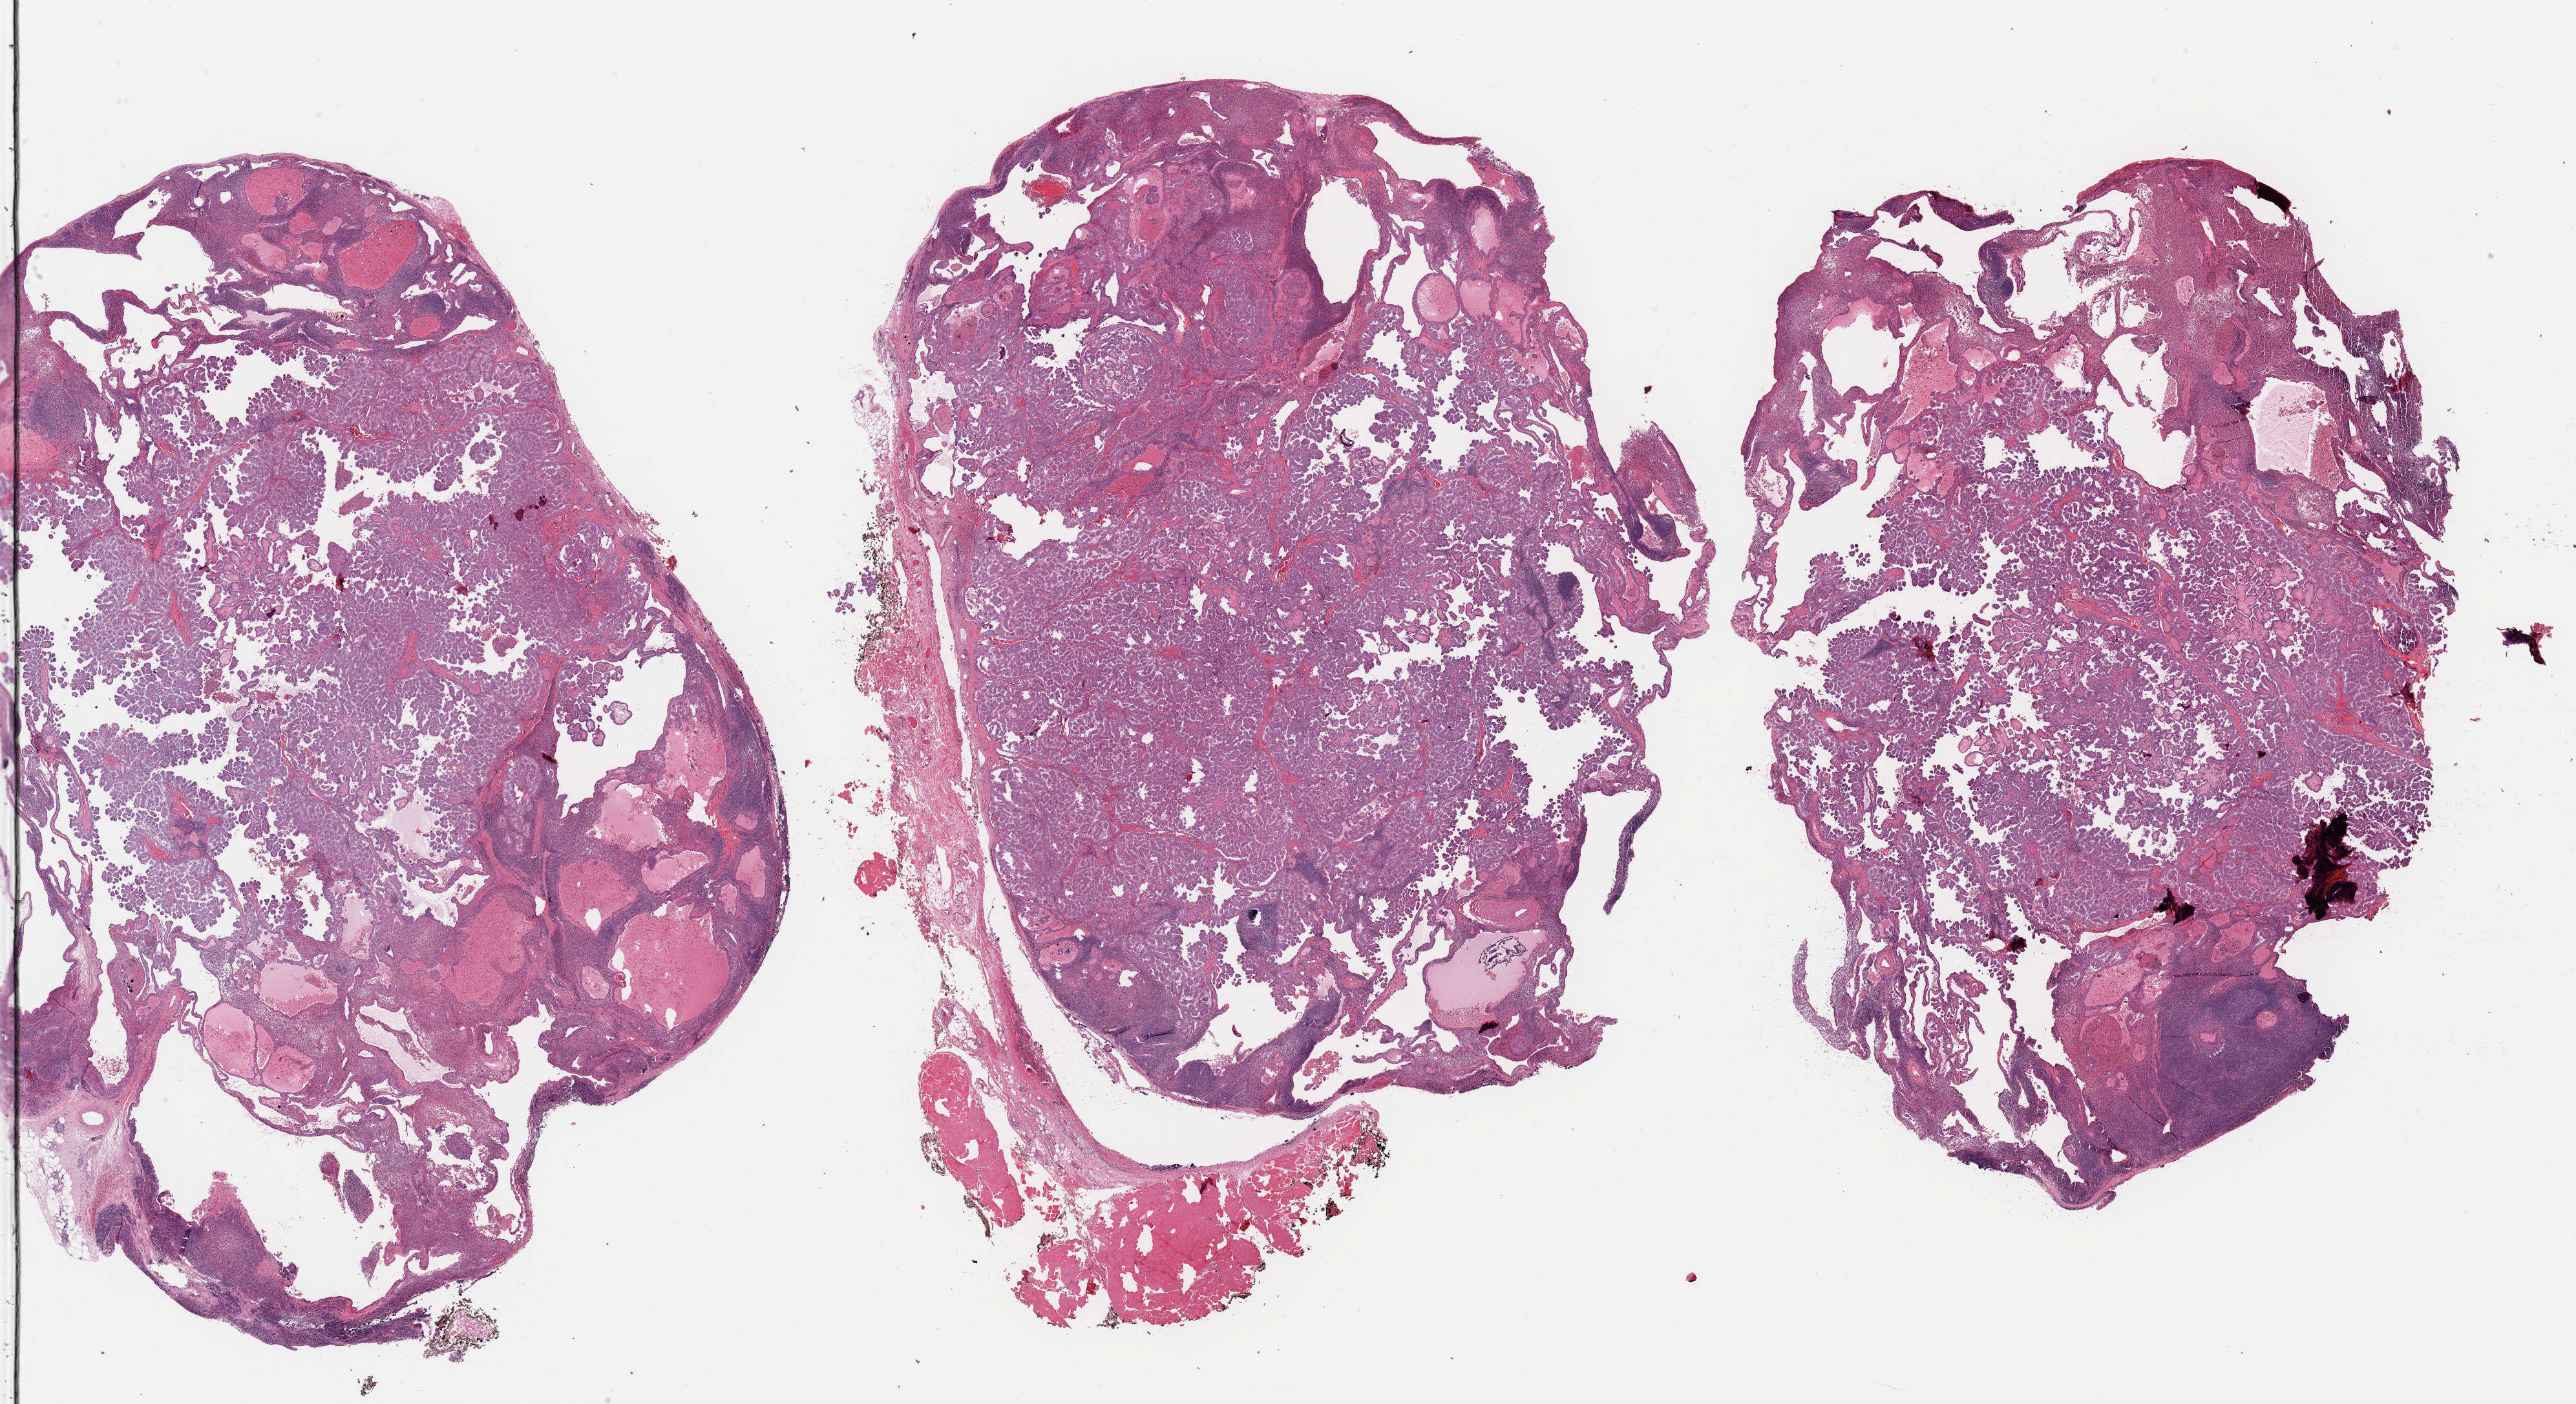
Digitized H&E tissue section (whole slide) — a low-resolution overview of the entire scanned area, about 31.5 x 17.2 mm; formalin-fixed paraffin-embedded (FFPE) diagnostic section; thyroid, primary tumour sample. Female, age 39 years at initial diagnosis.
- lymph nodes positive (case pathology): 1 of 1 examined
- AJCC pathologic stage: I
- histologic diagnosis: Papillary carcinoma, columnar cell (thyroid gland)